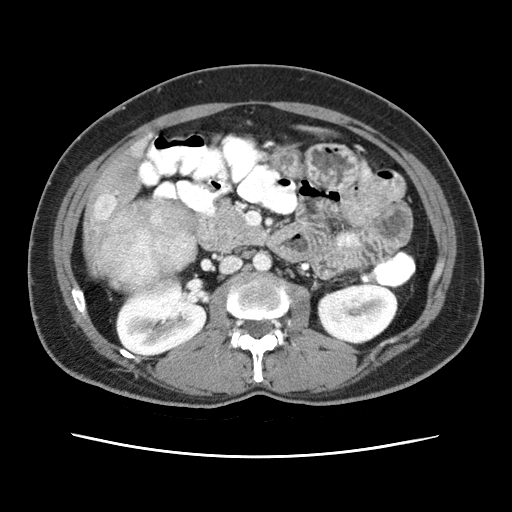
Contrast-enhanced abdominal CT (liver protocol), one axial slice; slice 10 of 79 in the series (ordered by position); soft-tissue window (W 400 / L 40 HU); 2.5 mm slice thickness; 512 × 512 image matrix. From the clinical record (not read from this slice): diagnosis: hepatocellular carcinoma (patient treated with transarterial chemoembolisation; whether this scan precedes or follows treatment is not stated here); TNM stage (as recorded): Stage-I; Child-Pugh class: A; tumour differentiation: moderately differentiated; tumour nodularity: uninodular.
Outlined on this slice (semi-automatic segmentation, software-assisted and operator-edited):
- abdominal aorta: bounding box [x1, y1, x2, y2] px = [253, 252, 272, 272]
- liver parenchyma outside the tumour (the mass and vessels are separate outlines, so this box may not span the whole liver): [86, 144, 143, 258]
- mass: [89, 197, 198, 293]